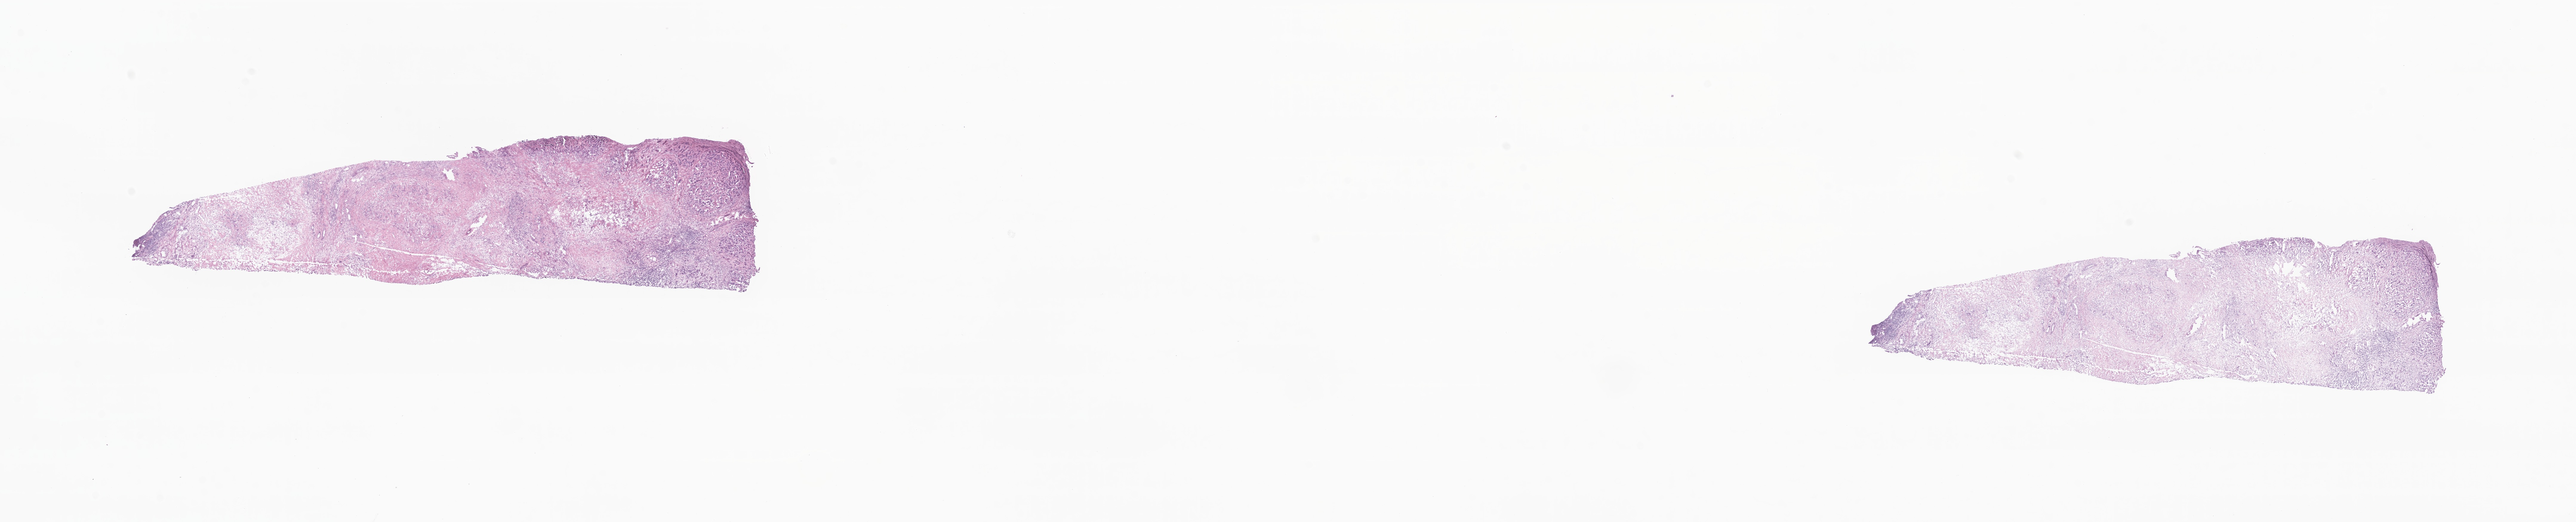
Haematoxylin and eosin whole-slide image, shown as a low-resolution overview of the whole scanned area (about 36.4 x 7.4 mm); cryosection; primary tumor; site: liver. Male patient; age at initial diagnosis 77 years. Slide review estimates, as recorded: tumor cells 19%, tumor nuclei 40%, stromal cells 53%, necrosis 0%, normal cells 28%. Infiltration values recorded for this section: lymphocyte infiltration 11%, monocyte infiltration 0%, neutrophil infiltration 0%.
Section: top of the tissue portion. Histologic diagnosis: Cholangiocarcinoma. AJCC pathologic stage: Stage II.